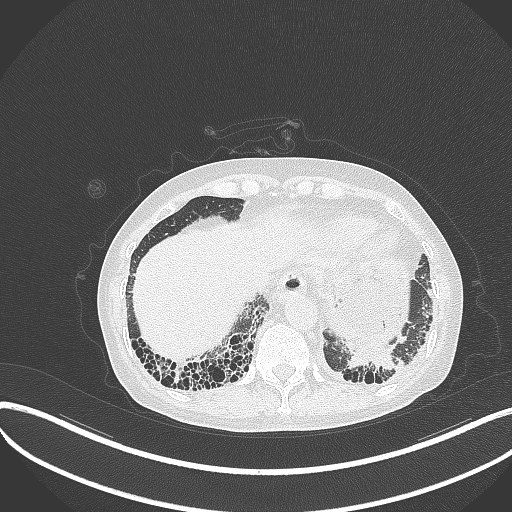
Chest CT, one axial slice; slice 56 of 373 in the series (ordered by position); reconstruction kernel B70f; 120 kVp; lung window (W 1500 / L -600 HU); 1 mm slice thickness; 512 × 512 image matrix. Female patient, age 56 years. Case-level facts recorded for this patient, not image findings: clinical TNM (as recorded): T1 N0 M0.
Outlined on this slice (bounding box drawn by a radiologist):
- lung tumour (recorded histology: adenocarcinoma): bounding box [x1, y1, x2, y2] px = [341, 344, 405, 375]